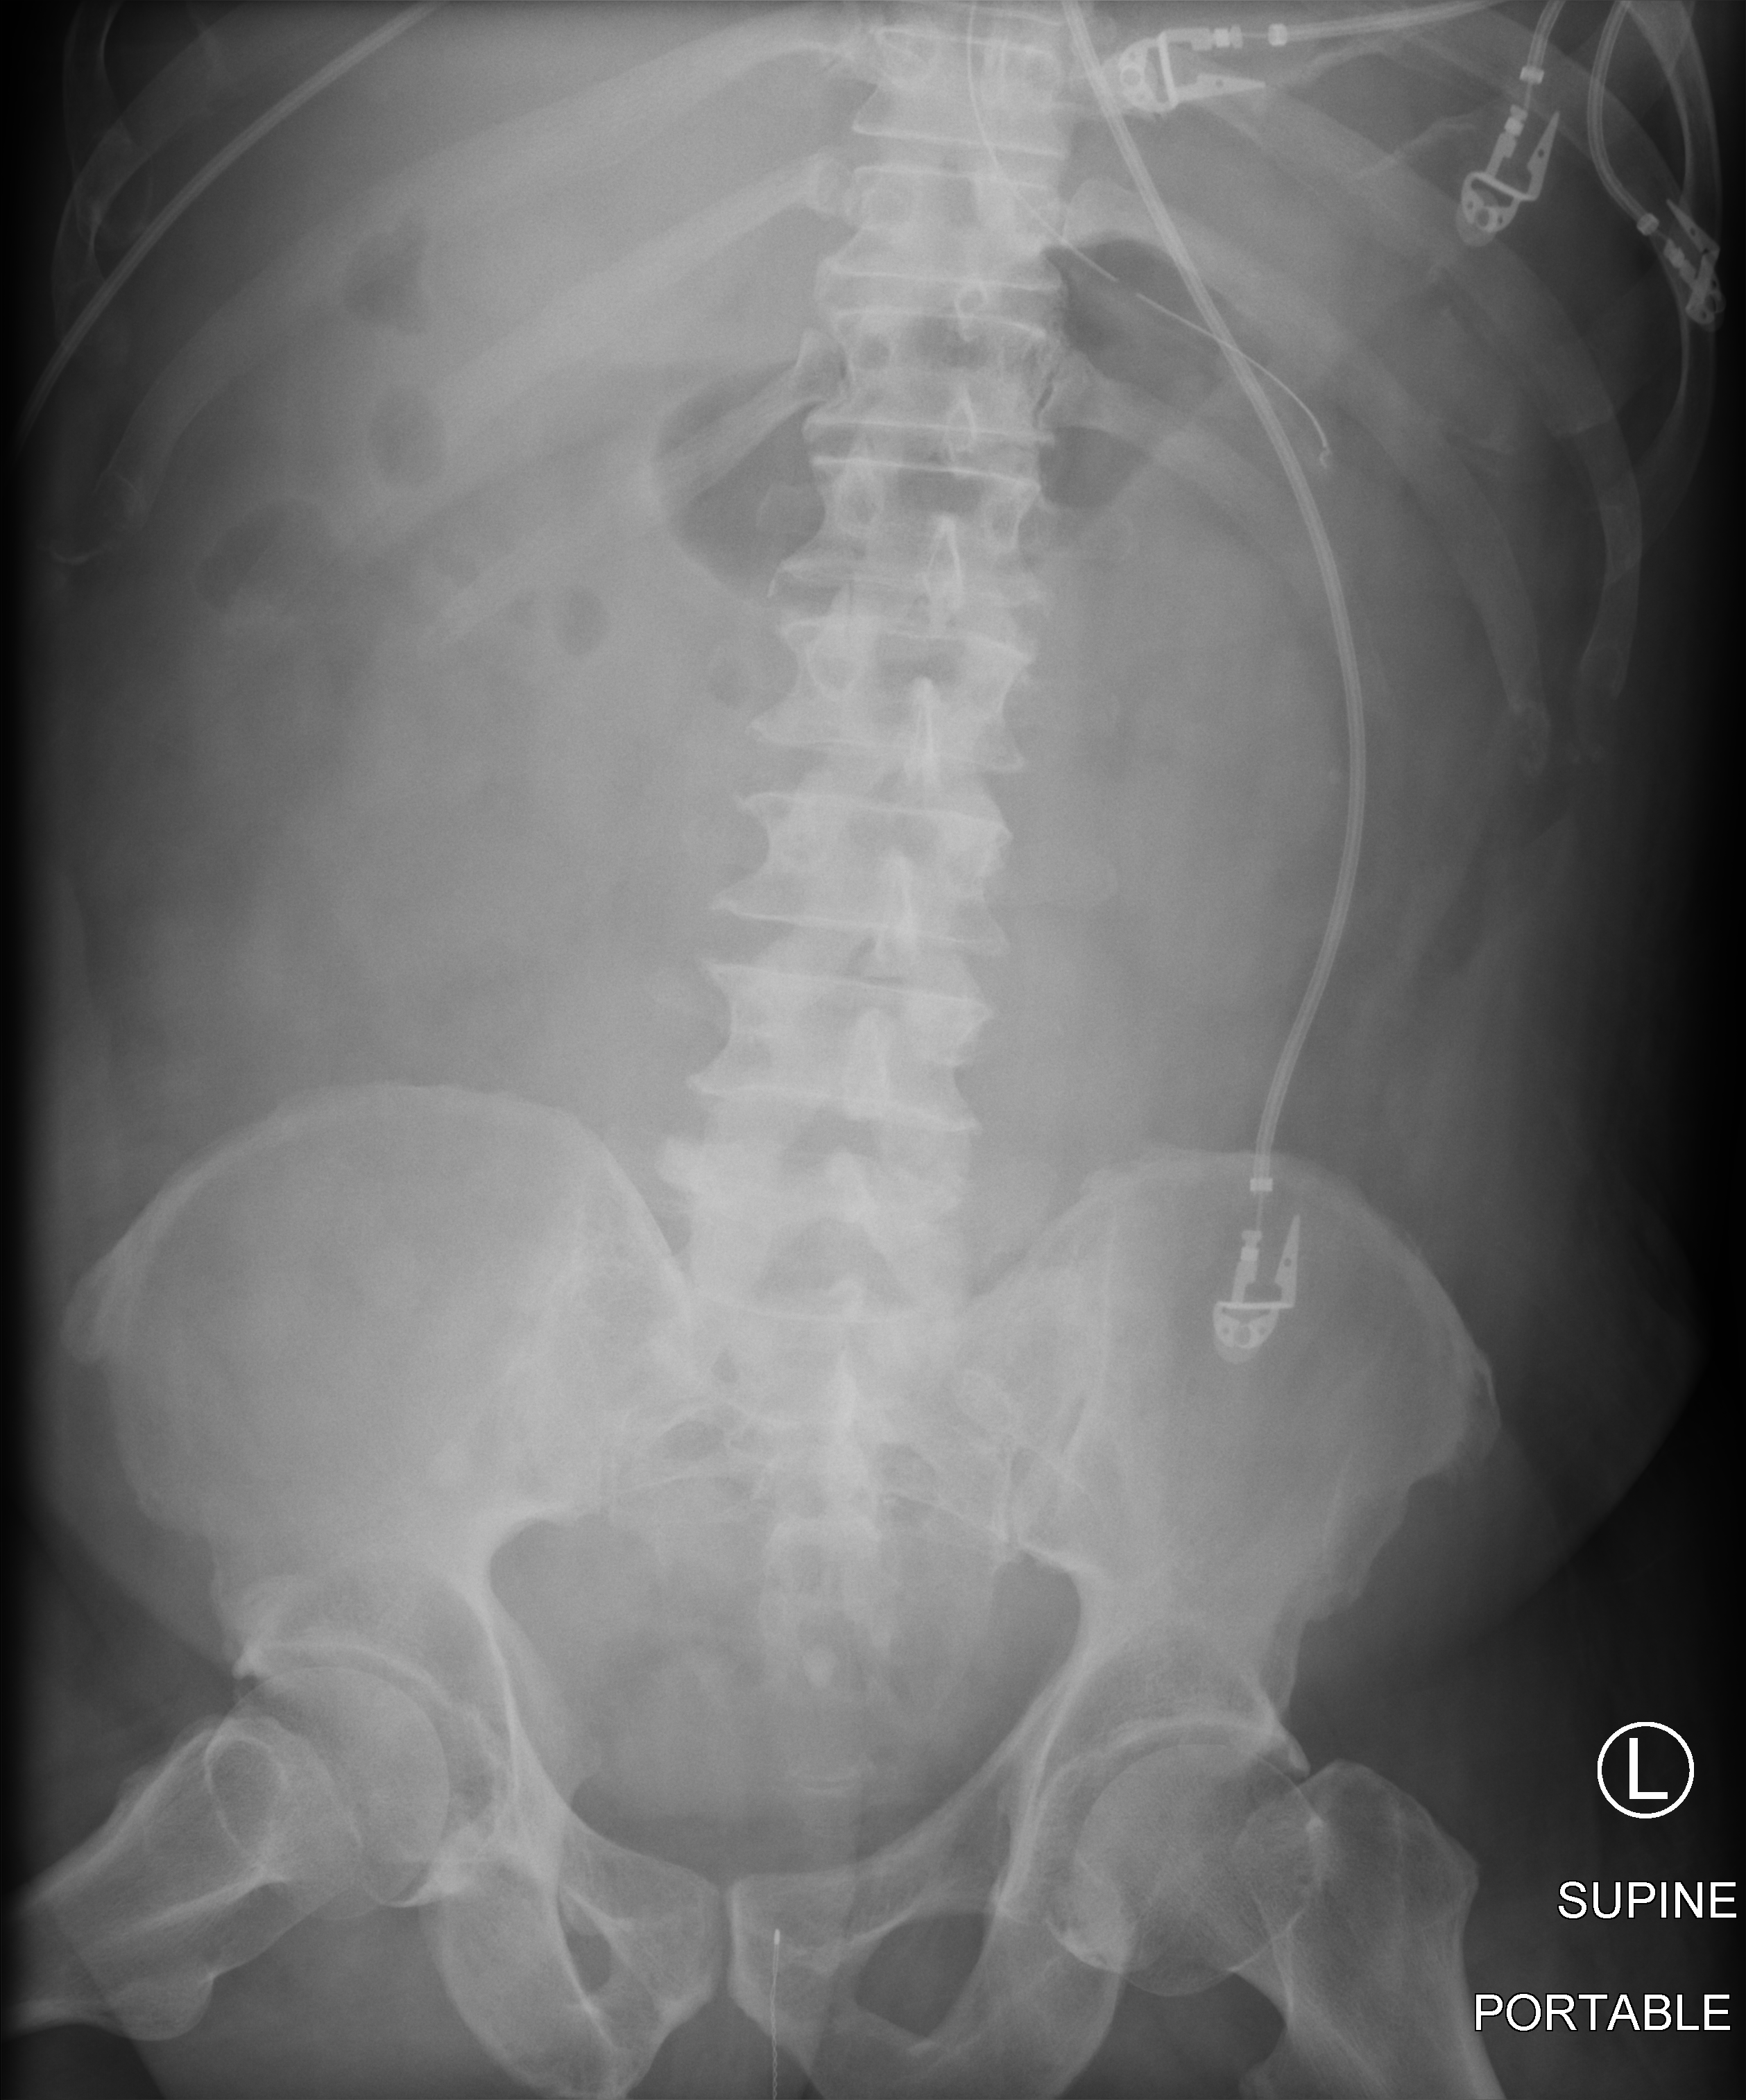
Bedside abdomen radiograph (computed radiography), anteroposterior (AP) projection. Male patient hospitalised with COVID-19, age 60–74 years.
Hospital-stay facts (about this admission, not read from this image; timing relative to this image not recorded): diabetes (admission record): no.